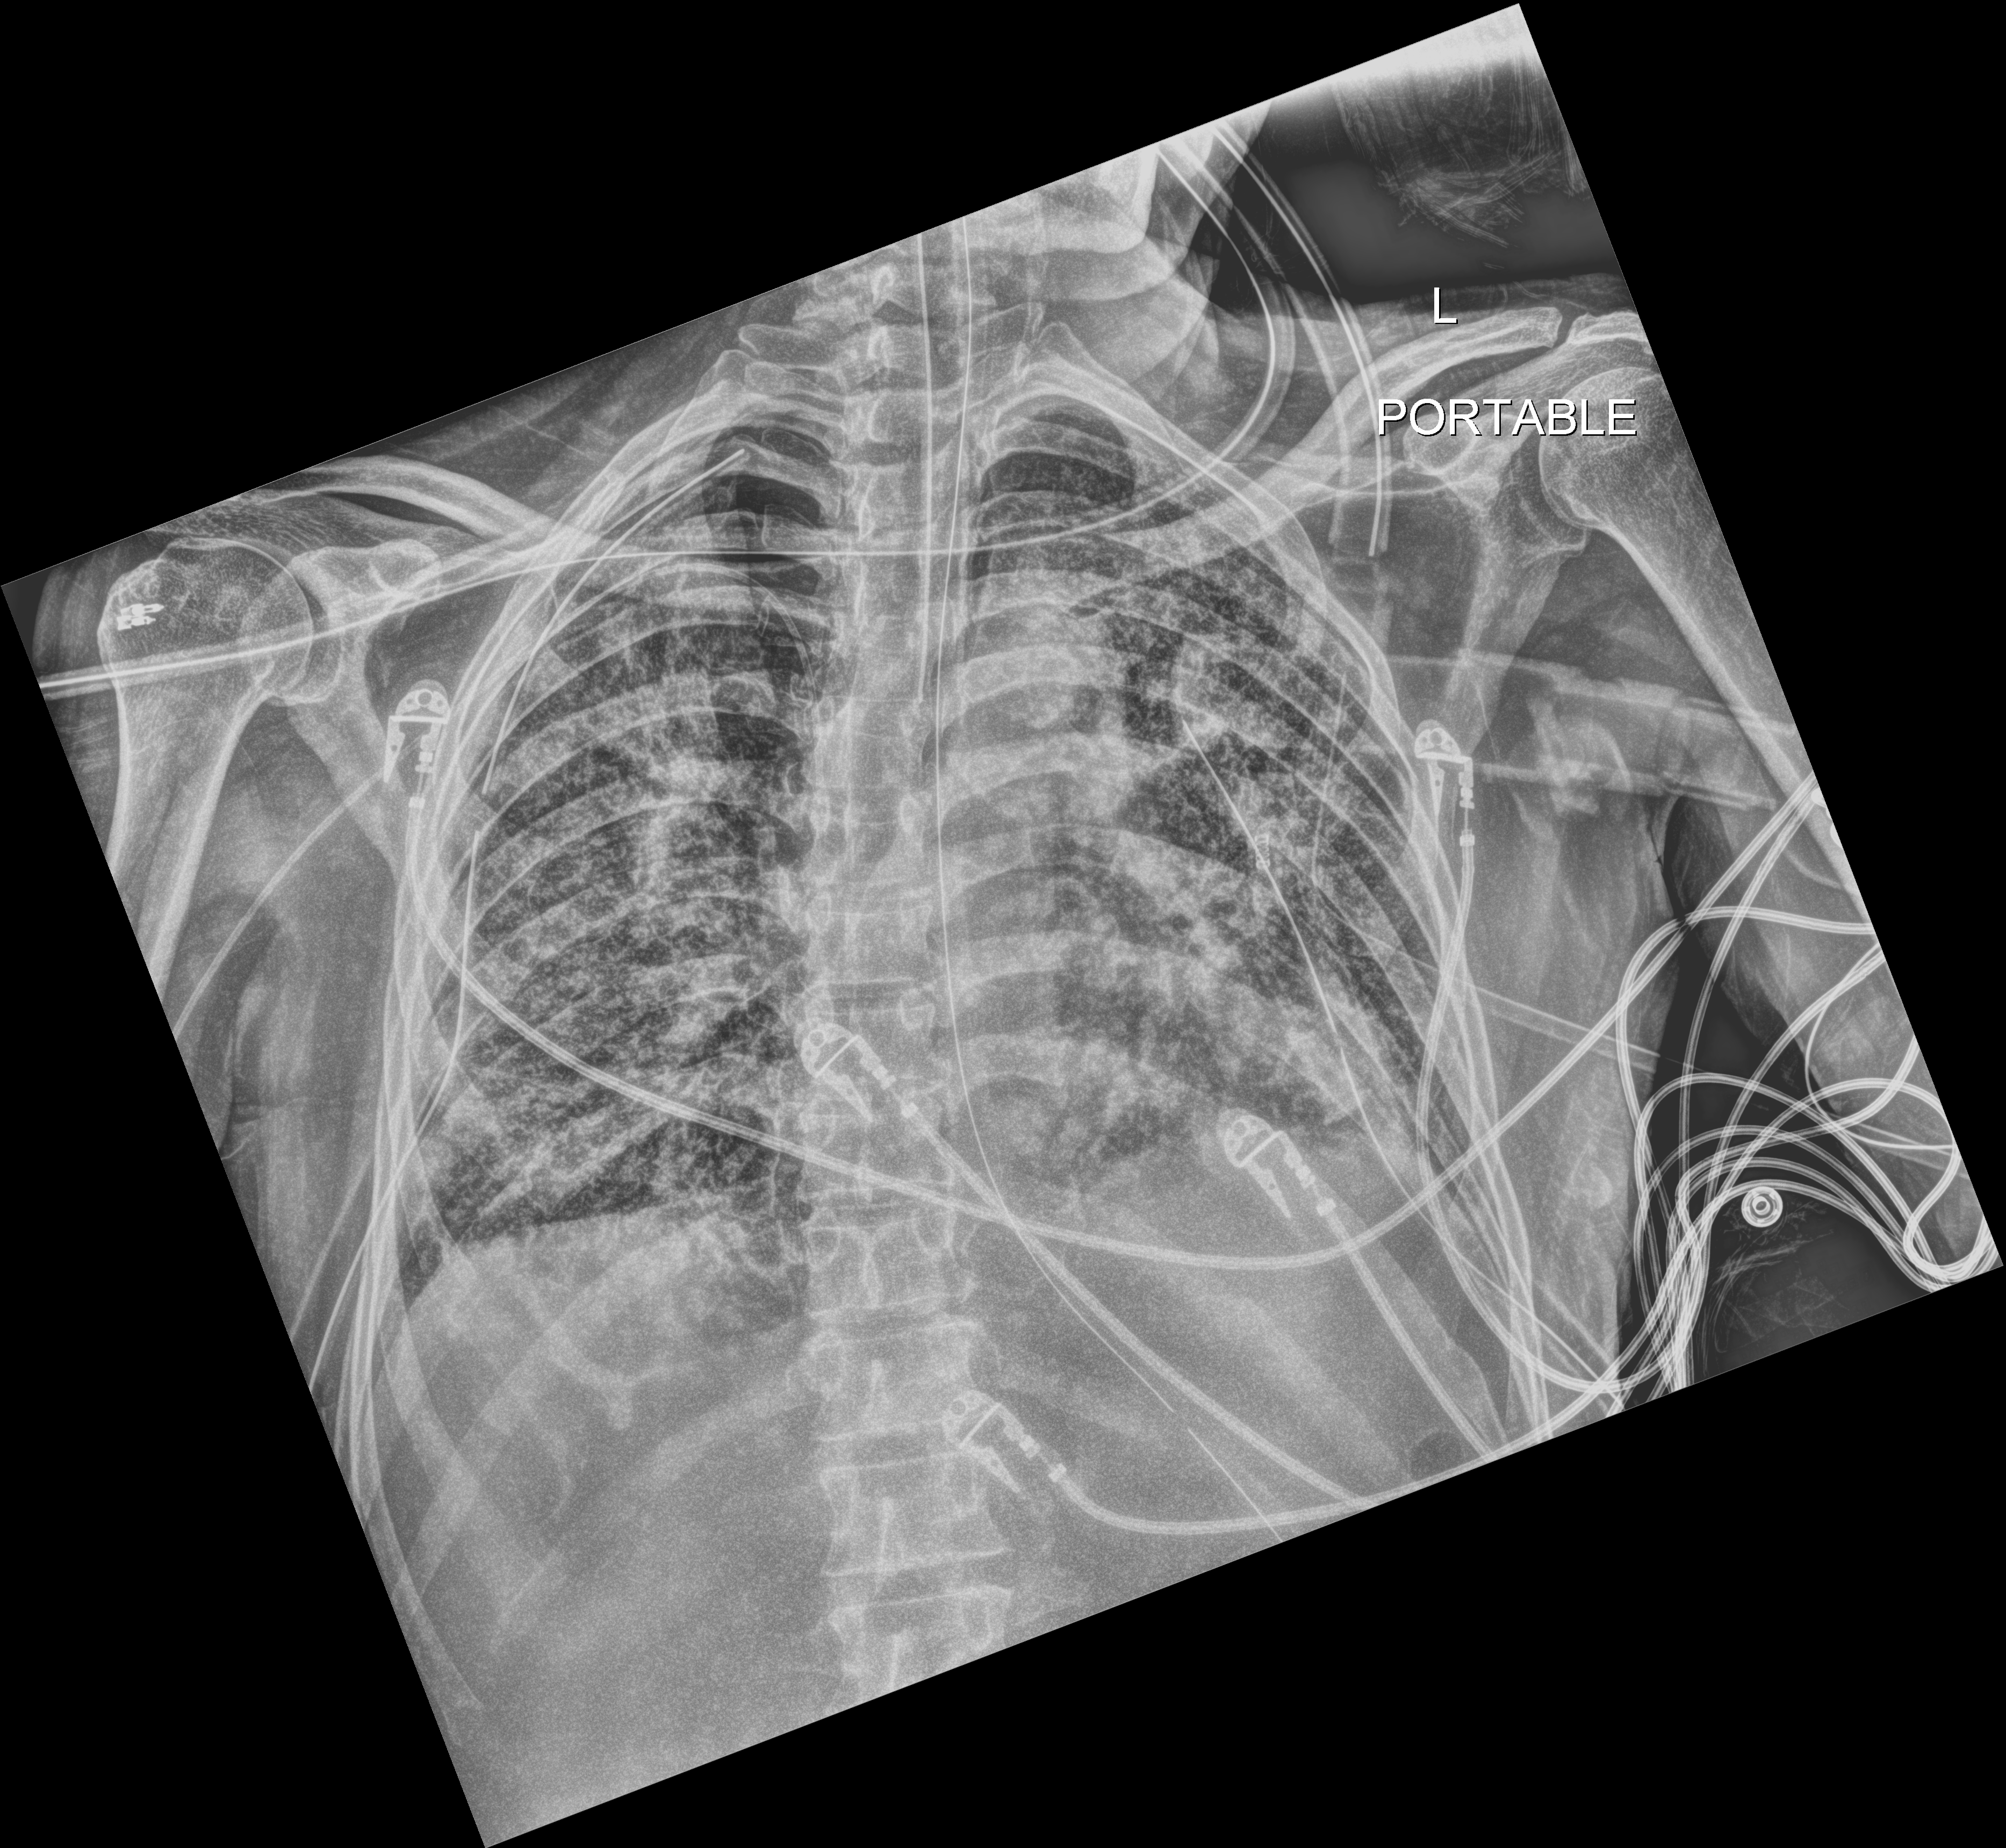
Bedside chest radiograph (digital radiography). Patient hospitalised with COVID-19; male, aged 60–74 years.
From the hospital-stay record, not from the radiograph (when in the stay this image was taken is not recorded): mechanically ventilated during this hospital stay: yes; admitted to intensive care during this hospital stay: yes; hypertension (admission record): no.